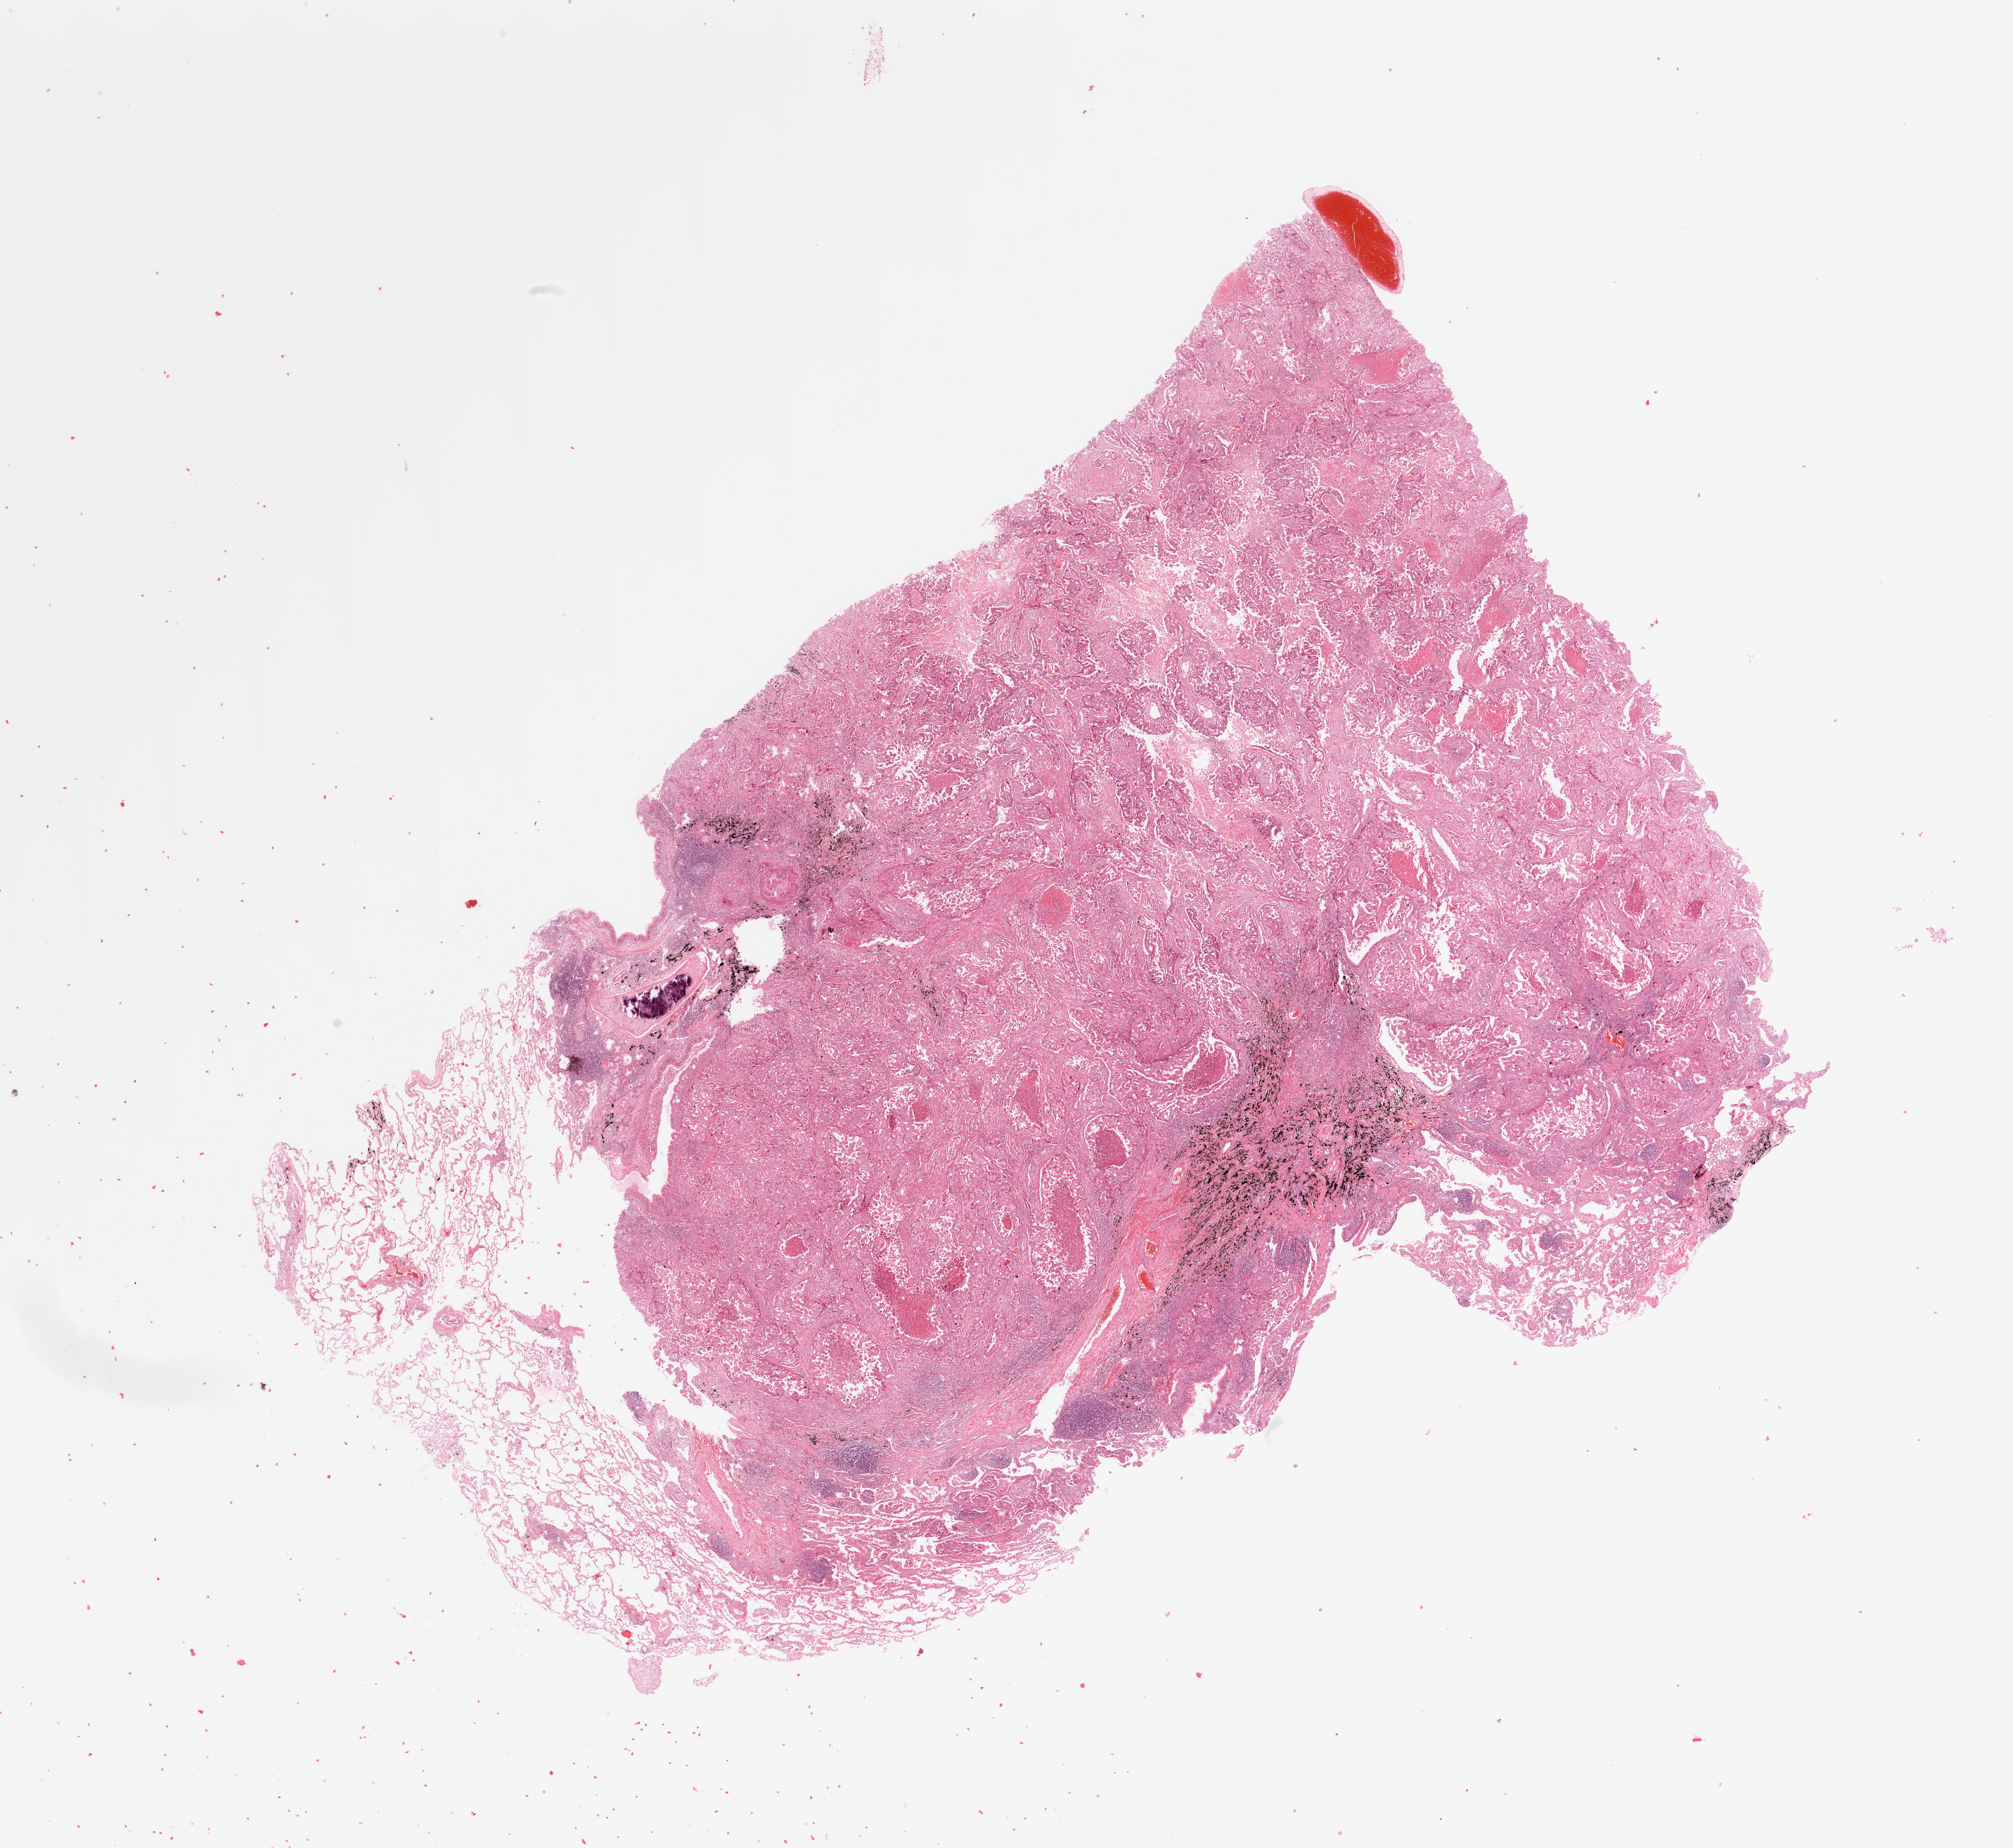
Digitized H&E tissue section (whole slide) — low-resolution overview of the scanned area, about 22.6 x 20.8 mm (slide scanned at 20x), tumour tissue sample, lung. 56-year-old male patient. Histologic grade: G3 (poorly differentiated).
AJCC pathologic stage: IB. Primary tumour site (as recorded): right upper lobe. Histologic diagnosis: Adenocarcinoma, NOS.